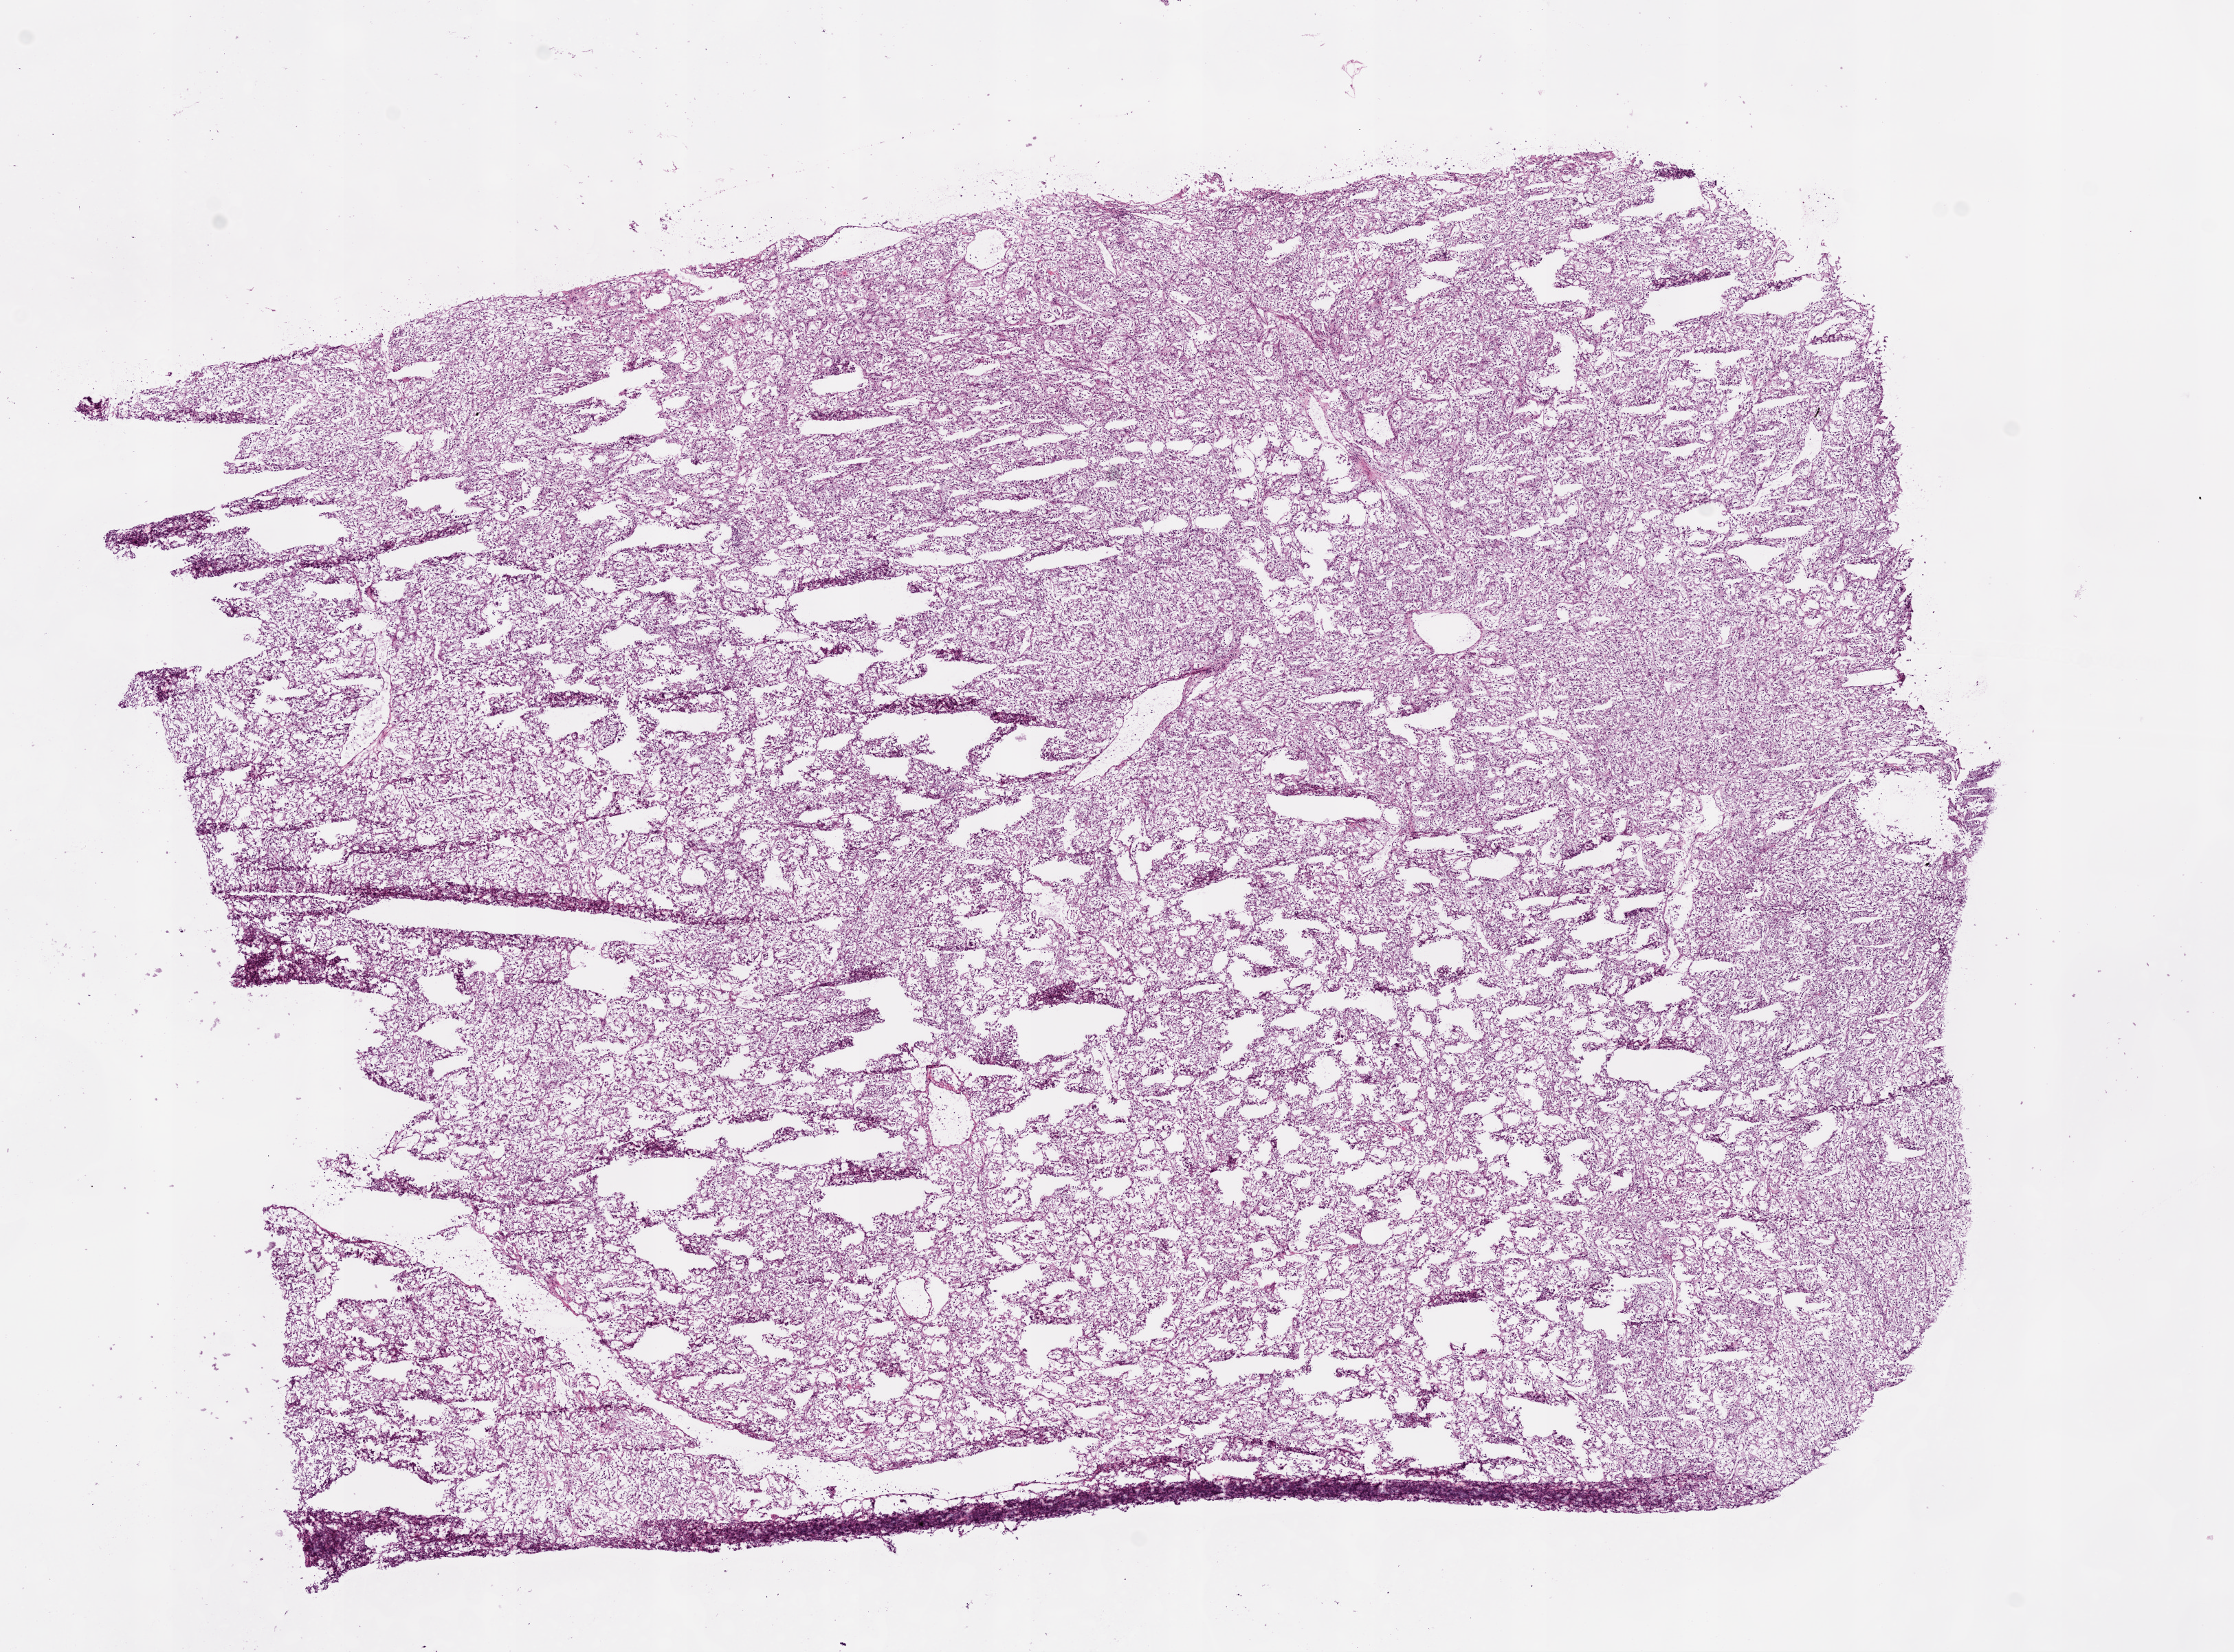
Hematoxylin and eosin (H&E) stained whole-slide image, shown as a low-resolution overview of the whole scanned area (about 13.0 x 9.6 mm, slide scanned at 20x). Frozen section from the bottom of the tissue portion. Sample: primary tumour, kidney. Patient: male, age at initial diagnosis 71 years. Histologic grade: G3 (poorly differentiated). Slide review estimates, as recorded: tumour cells 95%, tumour nuclei 85%, normal cells 0%, stromal cells 5%, necrosis 0%.
- pathologic diagnosis: Clear cell adenocarcinoma, NOS
- AJCC pathologic stage: III